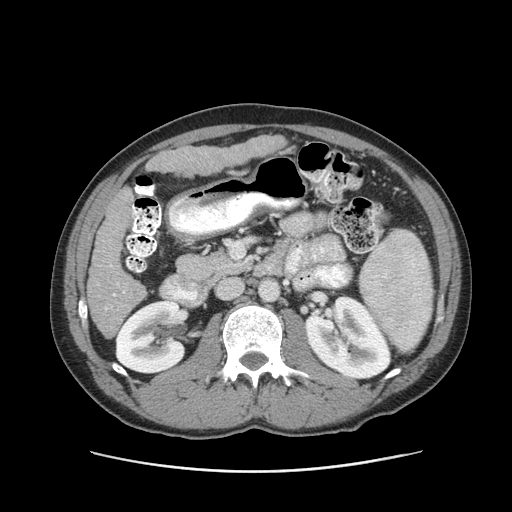
Contrast-enhanced abdominal CT (liver protocol), one axial slice; position 36 of 93 along the scan axis; reconstruction kernel STANDARD; 120 kVp; soft-tissue window (W 400 / L 40 HU); 512 × 512 image matrix, field of view 380 × 380 mm. Case-level facts recorded for this patient, not image findings: diagnosis: hepatocellular carcinoma (patient treated with transarterial chemoembolisation; whether this scan precedes or follows treatment is not stated here); TNM stage (as recorded): Stage-II; Child-Pugh class: A; tumour differentiation: moderately differentiated; tumour size: 1 cm.
Structures marked on this image (semi-automatic segmentation, software-assisted and operator-edited):
- liver parenchyma outside the tumour (the mass and vessels are separate outlines, so this box may not span the whole liver): bounding box <86,136,286,338> (left, top, right, bottom; pixels)
- liver vessels: <106,265,124,309>